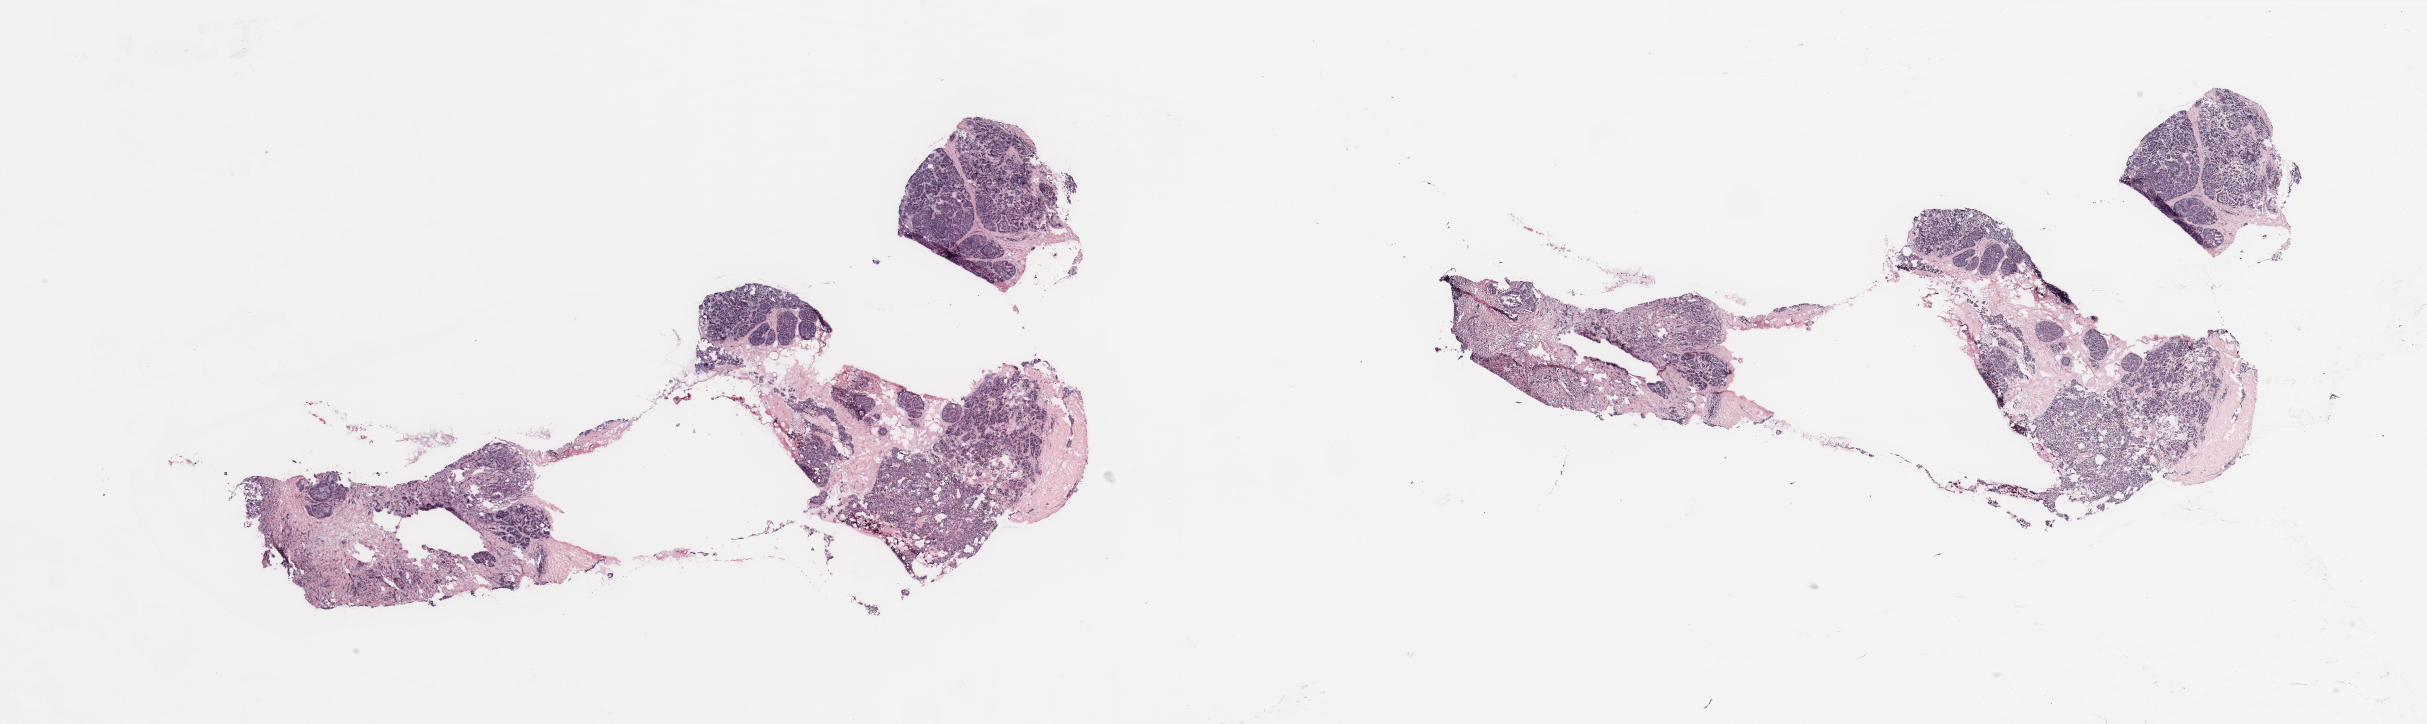
Digitized H&E tissue section (whole slide) — a low-resolution overview of the entire scanned area, about 38.4 x 11.5 mm (from a 20x scan). 52-year-old female patient.
- specimen: breast, tumour tissue